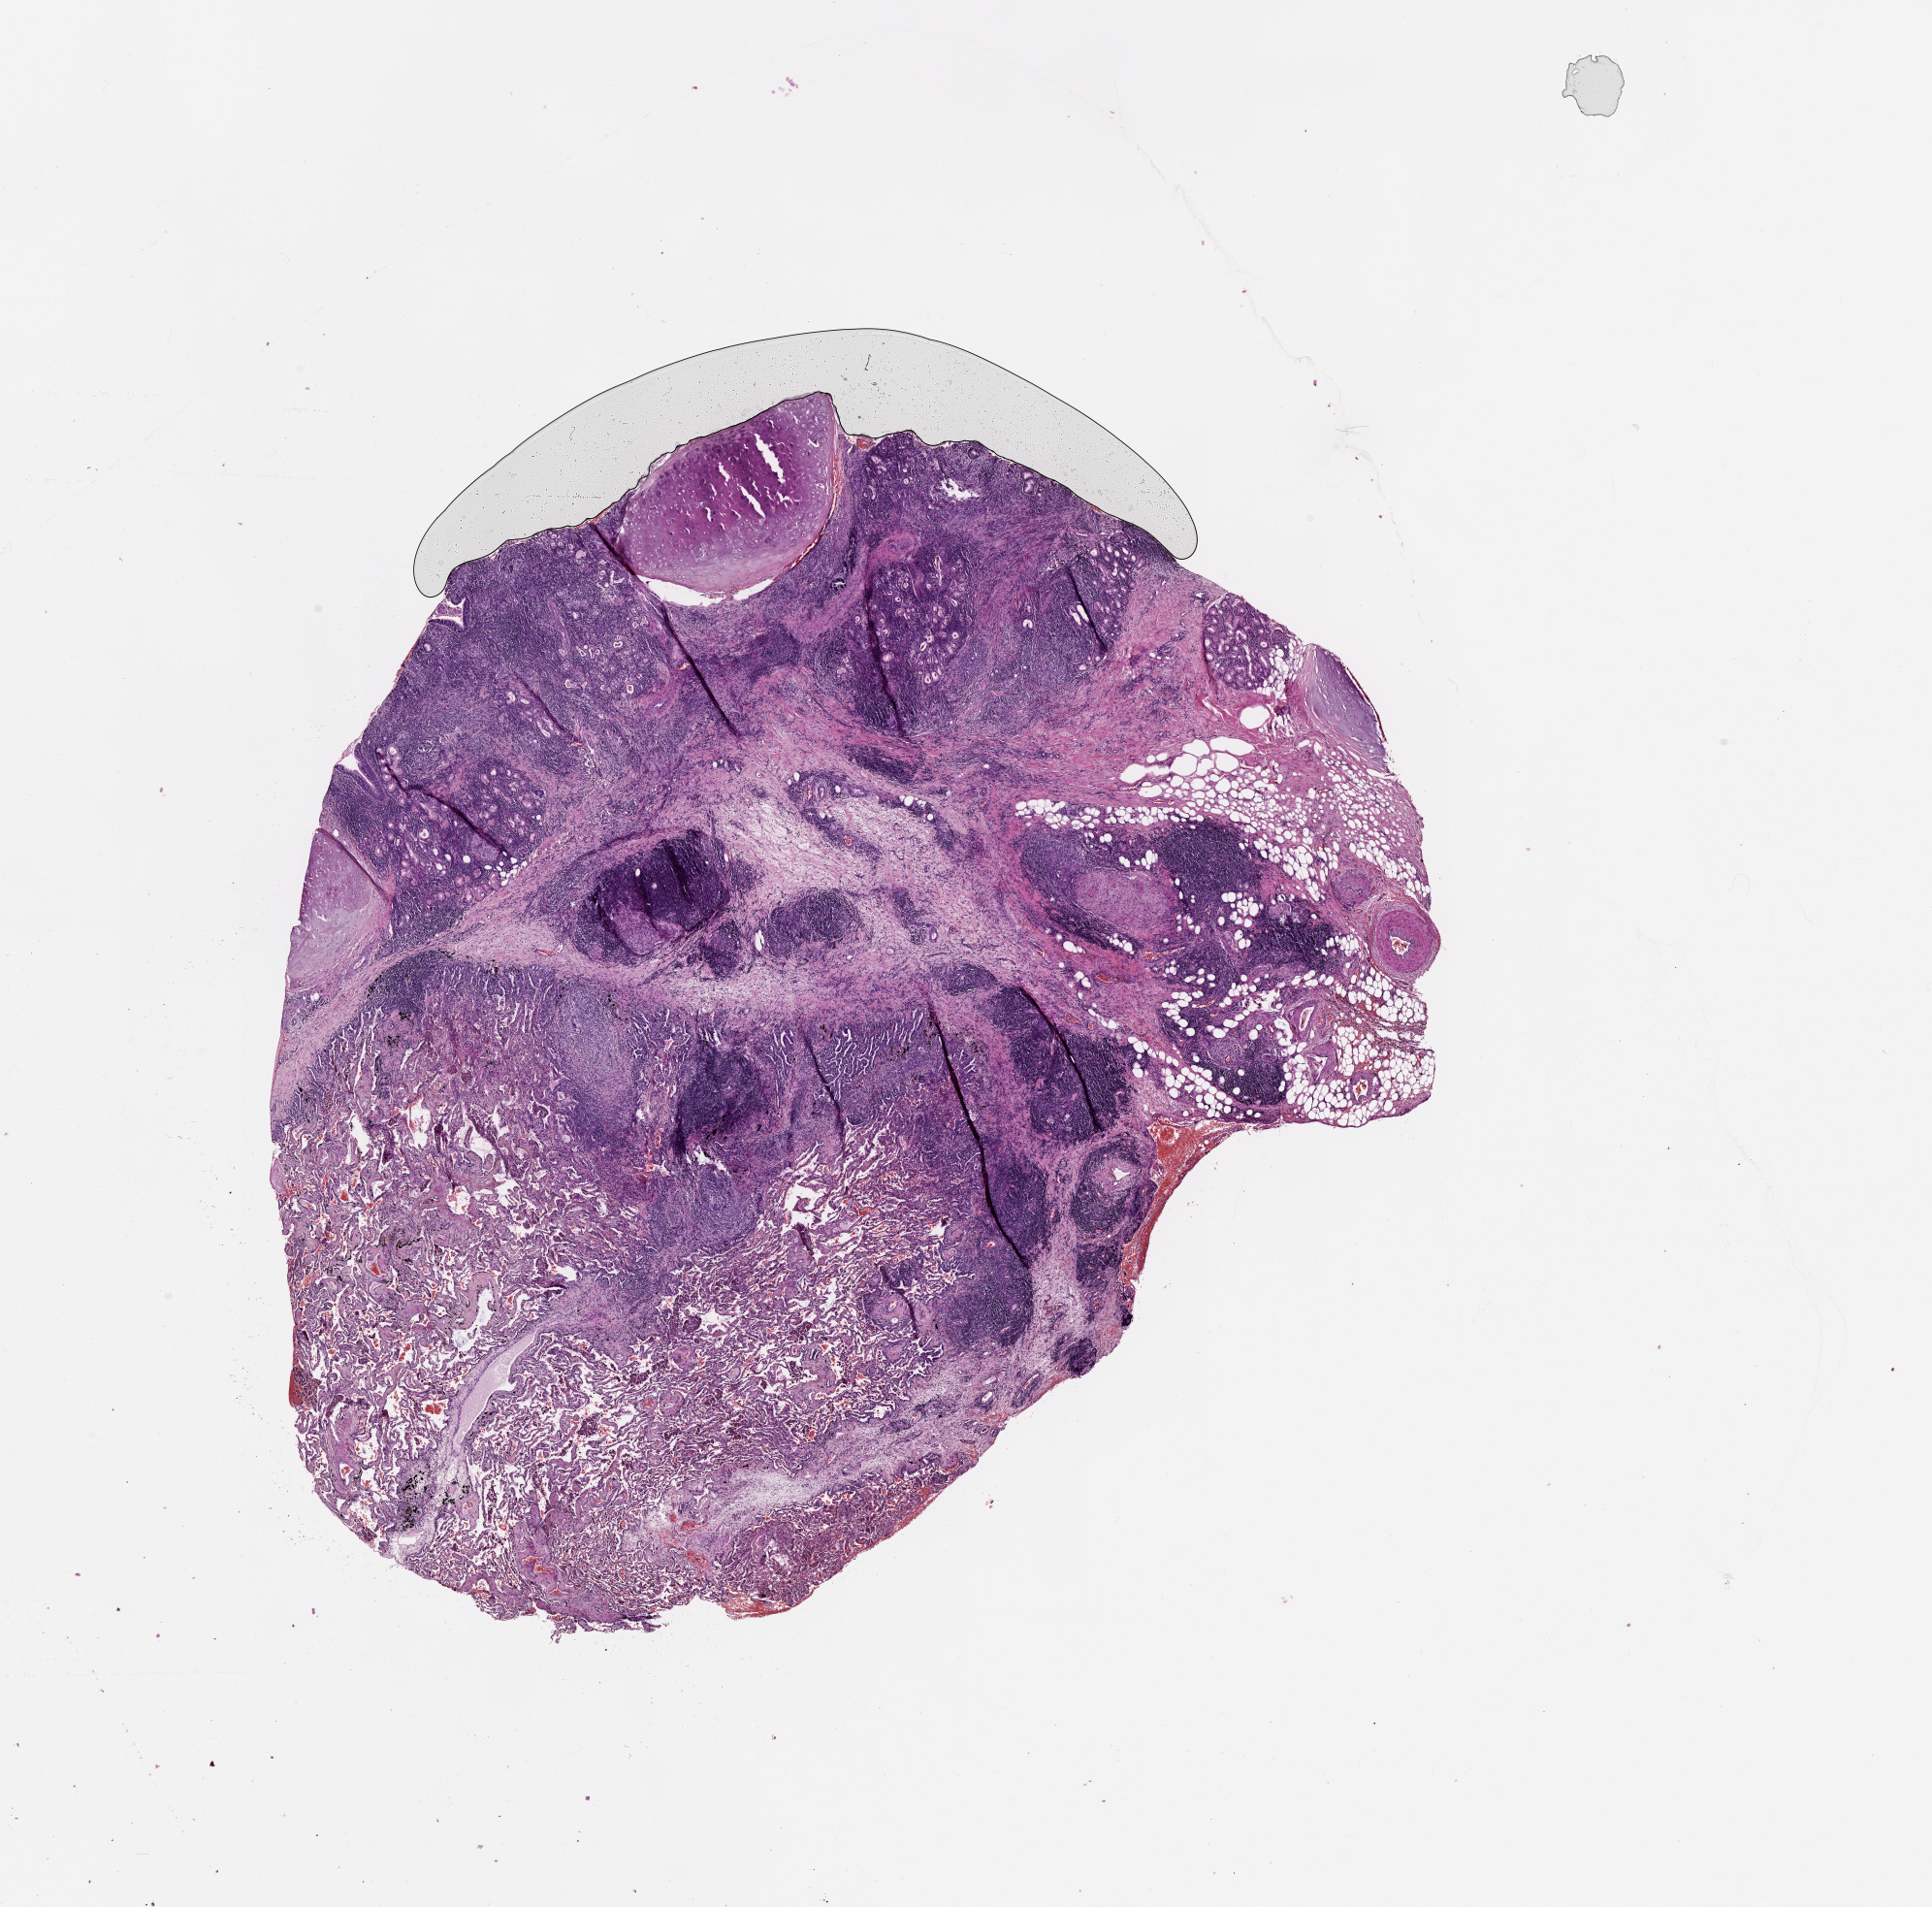
Whole-slide histology image, H&E — whole scanned area (about 16.0 x 15.8 mm, from a 20x scan) shown as a low-resolution overview; tumour tissue sample, lung. Patient: female, age 56 years.
• patient diagnosis (cohort enrolment): squamous cell carcinoma (lung)